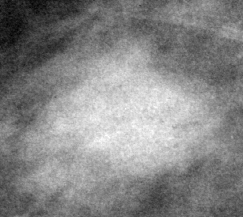
Cropped region of a digitized screen-film mammogram centred on a radiologist-marked abnormality; right breast; MLO view; BI-RADS breast density category 2 (scale 1–4).
Mass, shape lobulated, margins circumscribed / obscured; BI-RADS assessment category 4; subtlety rating 4 on a 1 (subtle) to 5 (obvious) scale; pathology result (as recorded, not read from the image): benign.